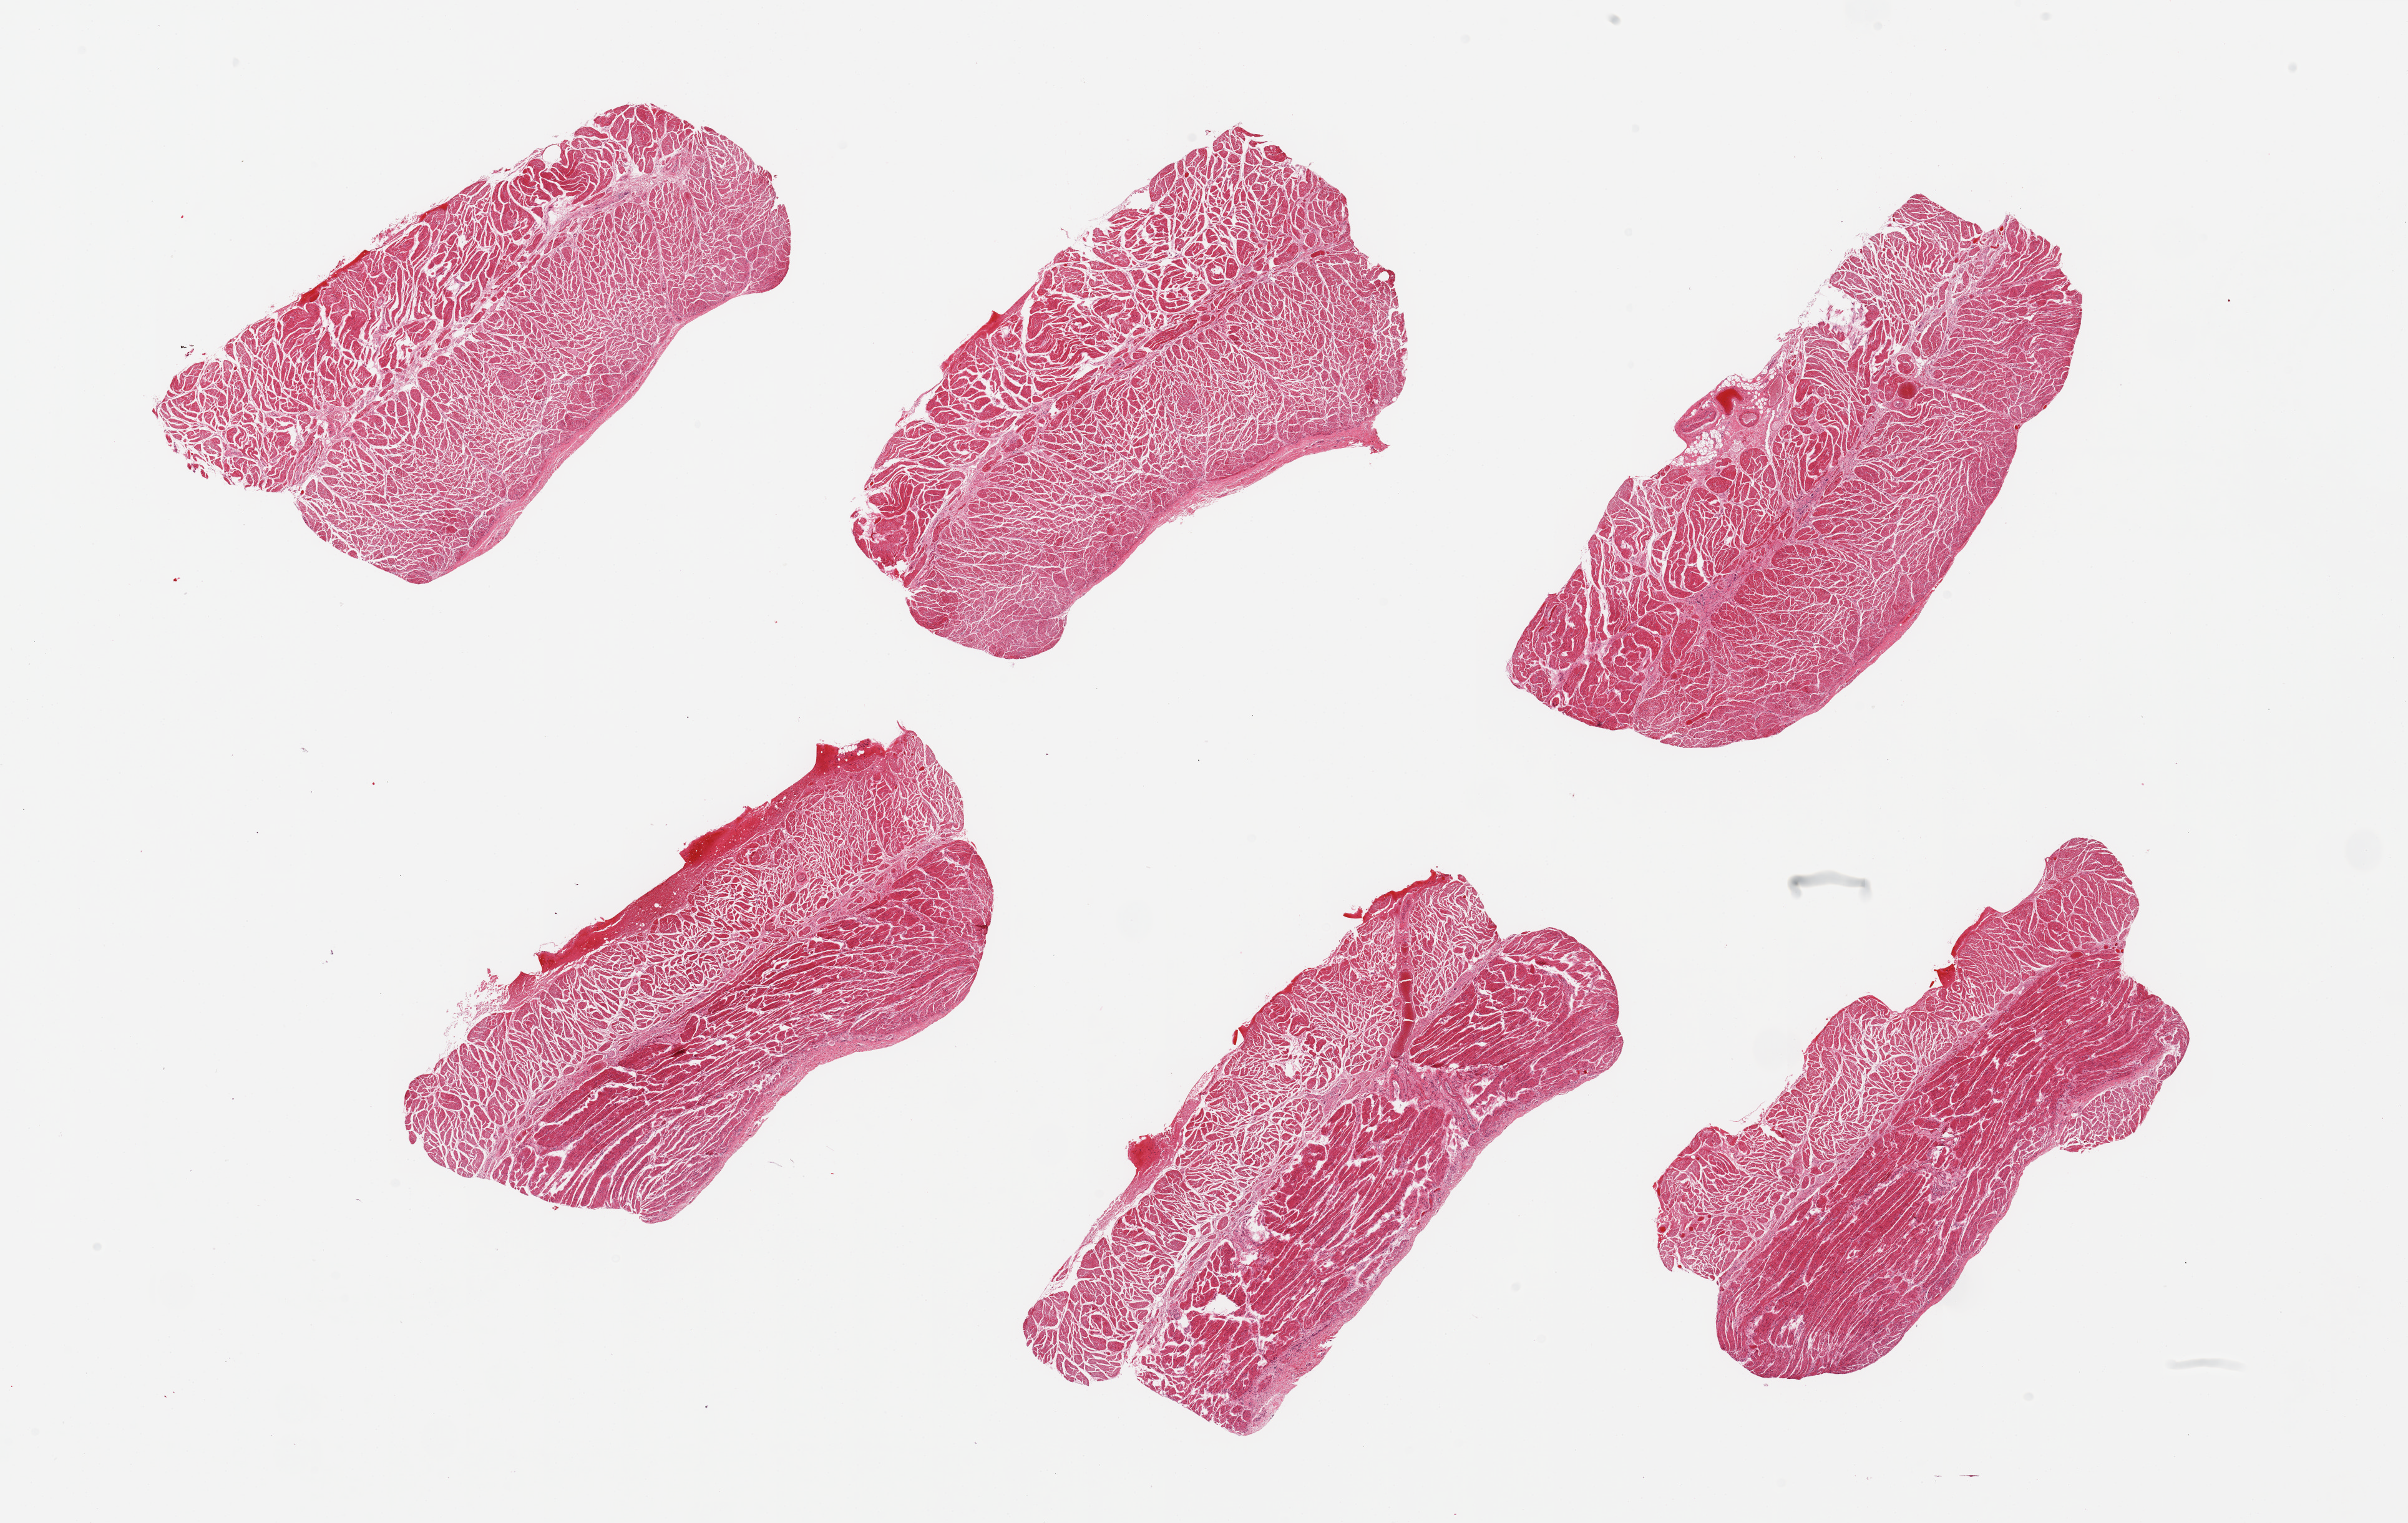
Whole-slide image, haematoxylin and eosin stain, brightfield, a low-resolution overview of the entire scanned area, about 30.5 x 19.3 mm (slide scanned at 20x), PAXgene-fixed paraffin-embedded (PFPE) section, sampled site (target tissue): esophageal muscle, donor tissue sample. Donor sex: male.
Pathologist's review note for this sample: 6 pieces; well trimmed.